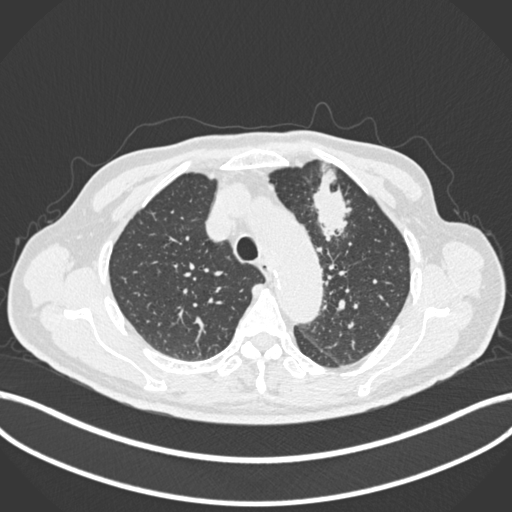
Chest CT, one axial slice. Position 194 of 261 along the scan axis. Reconstruction kernel B30f. Lung window (W 1500 / L -600 HU). 512 × 512 image matrix, field of view 400 × 400 mm. Patient: male, 74 years. Case-level facts recorded for this patient, not image findings: clinical TNM (as recorded): T2b N0 M1c.
Outlined on this slice (bounding box drawn by a radiologist):
- lung tumour (recorded histology: adenocarcinoma): bounding box <308,162,358,245> (left, top, right, bottom; pixels)